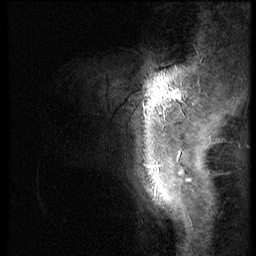
Breast MRI (dynamic contrast-enhanced), one sagittal slice; slice 9 of 56 in the series (ordered by position); 3 images stored at this slice position (order not interpretable as contrast timing); 1.5 T; TE 4.2 ms, TR 9 ms; 256 × 256 image matrix. Female patient, age 46 years. Case-level facts recorded for this patient, not image findings: setting: breast cancer imaged before/during neoadjuvant chemotherapy; receptor status: HER2-positive.
Structures marked on this image (semi-automatically segmented with operator editing):
- analysis volume of interest (the breast-tissue region the enhancement analysis was run in; not a lesion): bounding box <95,68,190,143> (left, top, right, bottom; pixels)
- tumour enhancement mask (voxels above the 140 % enhancement threshold inside the analysis volume of interest): <172,92,180,100>